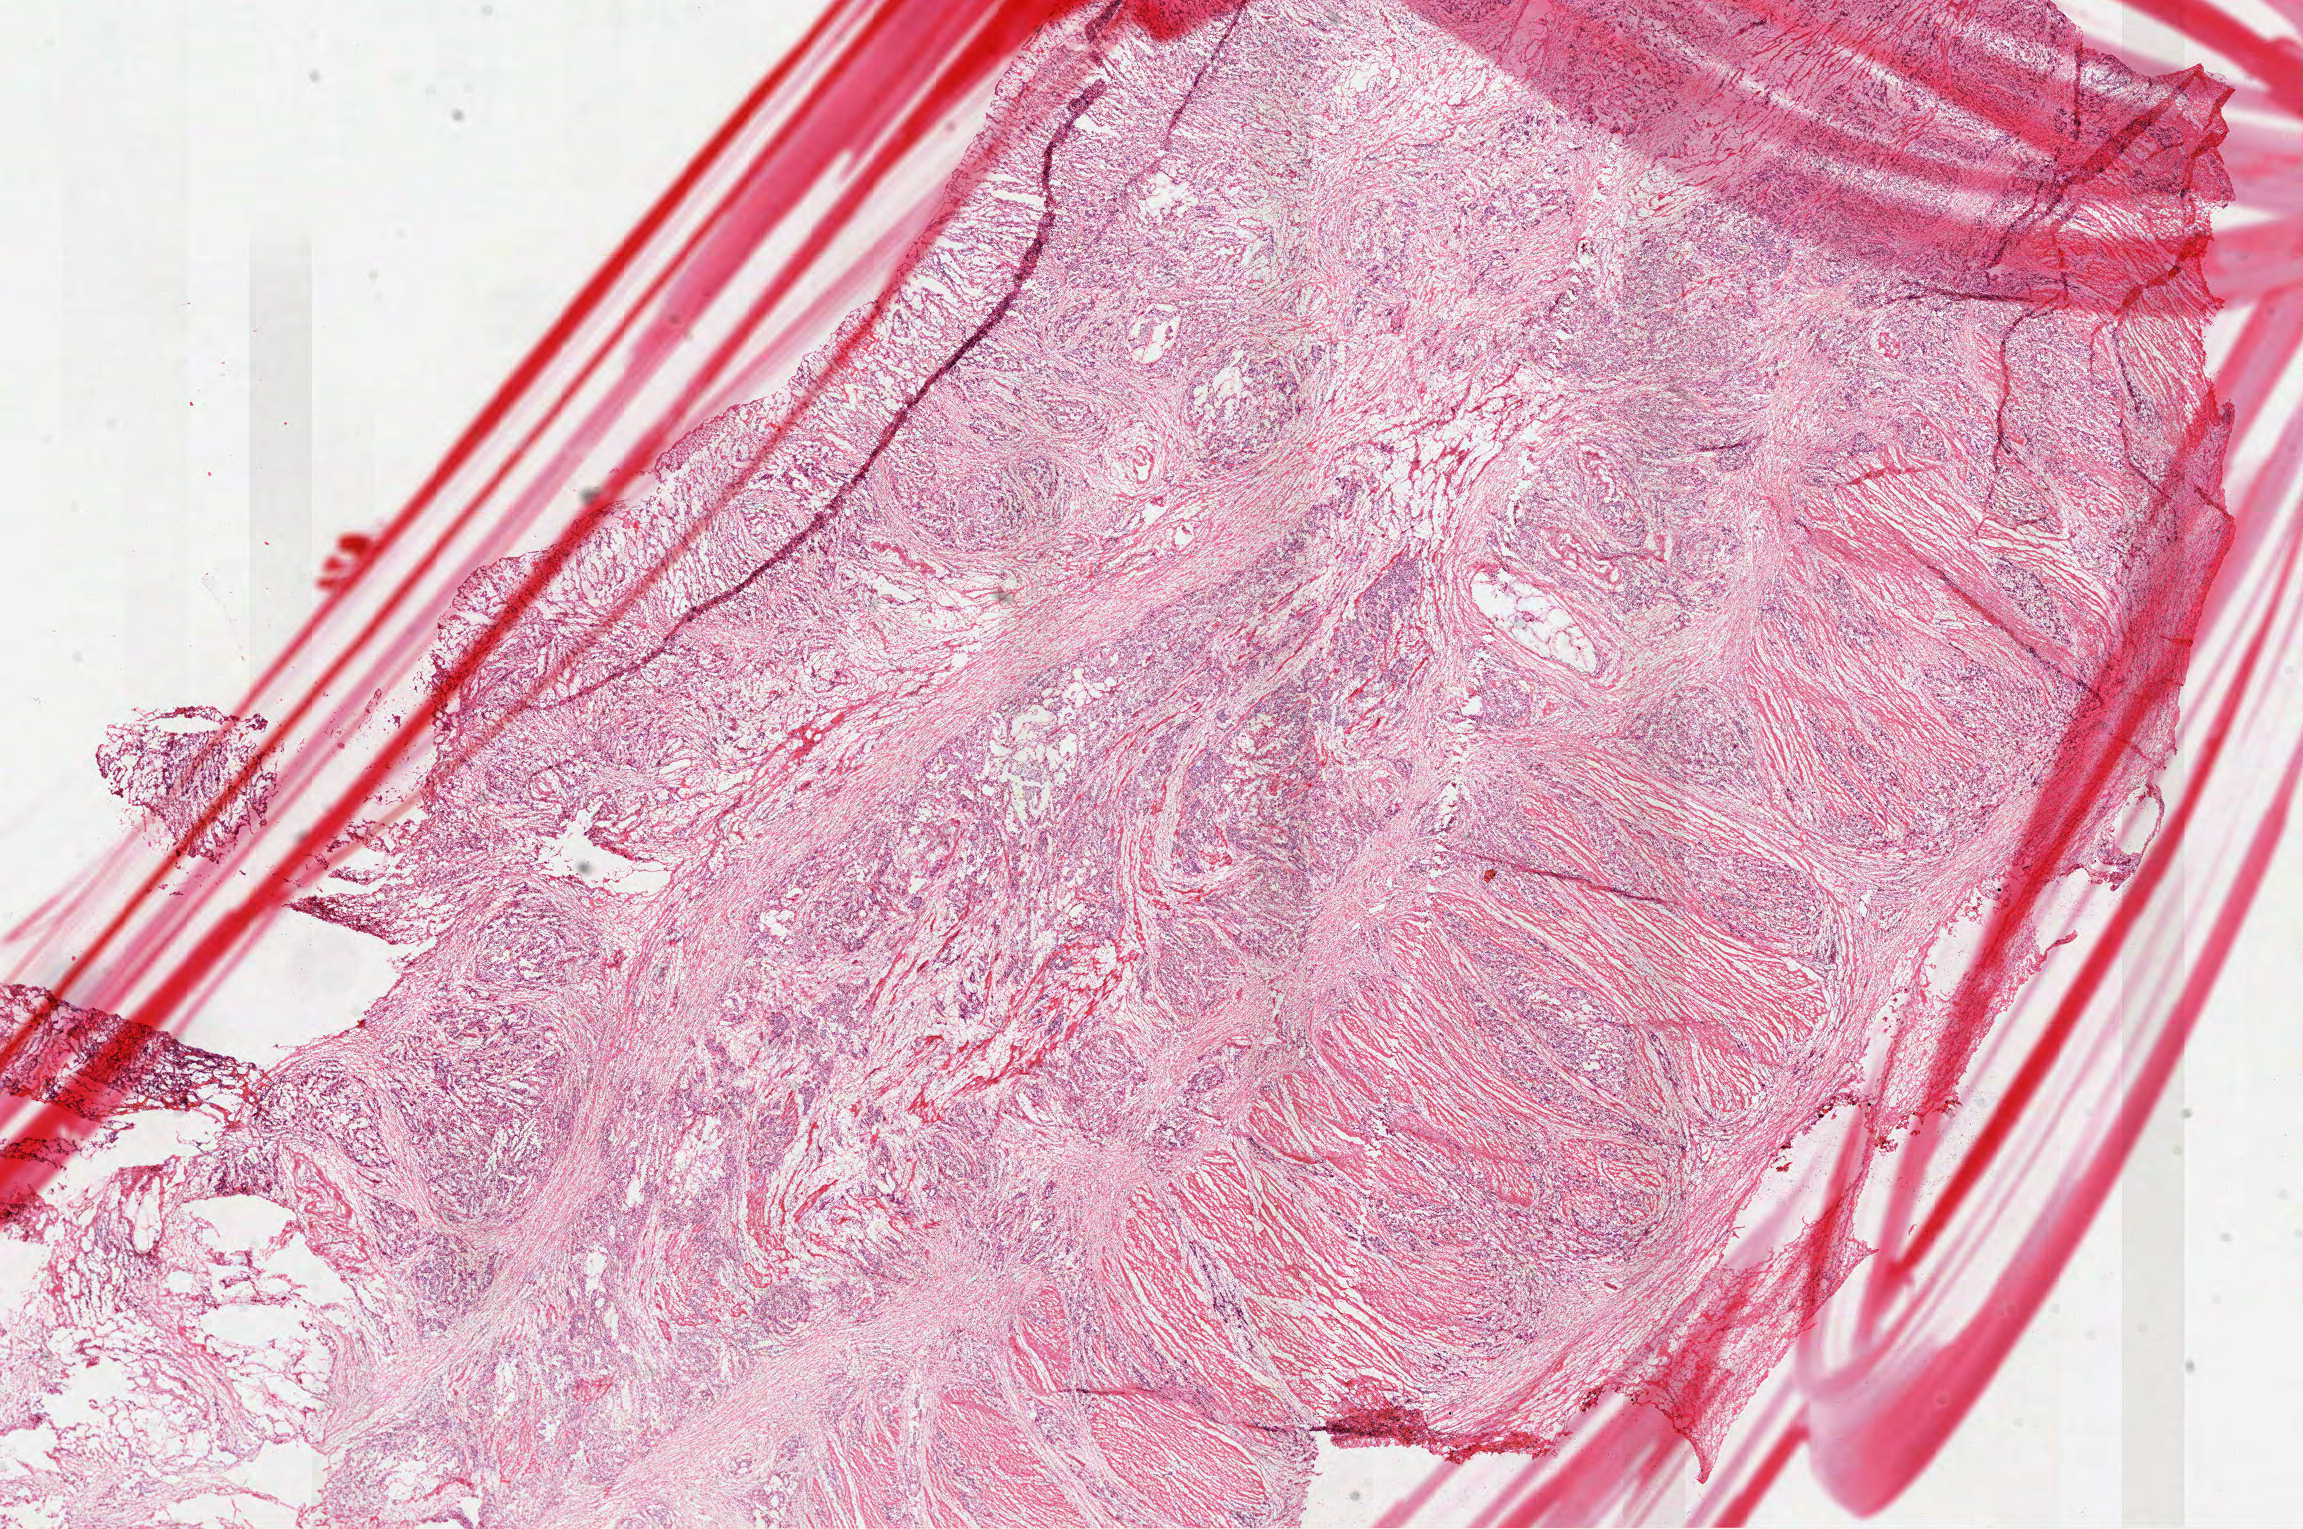
Whole-slide histology image, H&E — shown as a low-resolution overview of the whole scanned area (about 18.6 x 12.3 mm); frozen section; primary tumour sample from the rectum. Patient: female, age at initial diagnosis 77 years. Slide review estimates, as recorded: tumour cells 98%, tumour nuclei 75%, normal cells 0%, stromal cells 0%, necrosis 2%. Infiltration values recorded for this section: lymphocyte infiltration 5%, monocyte infiltration 0%, neutrophil infiltration 2%.
- lymph nodes positive (case pathology): 4 of 4 examined
- histologic diagnosis: Adenocarcinoma, NOS (rectosigmoid junction)
- AJCC pathologic stage: IIIC (7th edition)